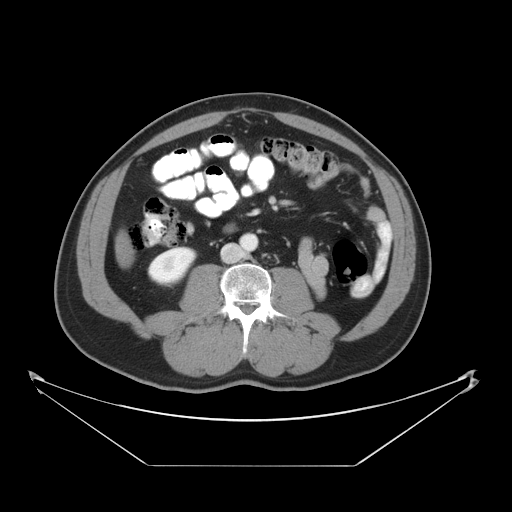
Contrast-enhanced abdominal CT, one axial slice; slice 9 of 46 in the series (ordered by position); reconstruction kernel STANDARD; soft-tissue window (W 400 / L 40 HU); 512 × 512 image matrix, field of view 465 × 465 mm. Male patient, age 57 years. From the clinical record (not read from this slice): diagnosis: colorectal cancer liver metastases, imaged before liver resection; multiple liver metastases: no; largest metastasis: 3.3 cm; chemotherapy before resection: yes.
Outlined on this slice (expert manual segmentation):
- liver: bounding box (x1, y1, x2, y2) in pixels: (122, 241, 128, 252)
- planned liver remnant (the part of the liver to remain after resection): (122, 249, 128, 252)